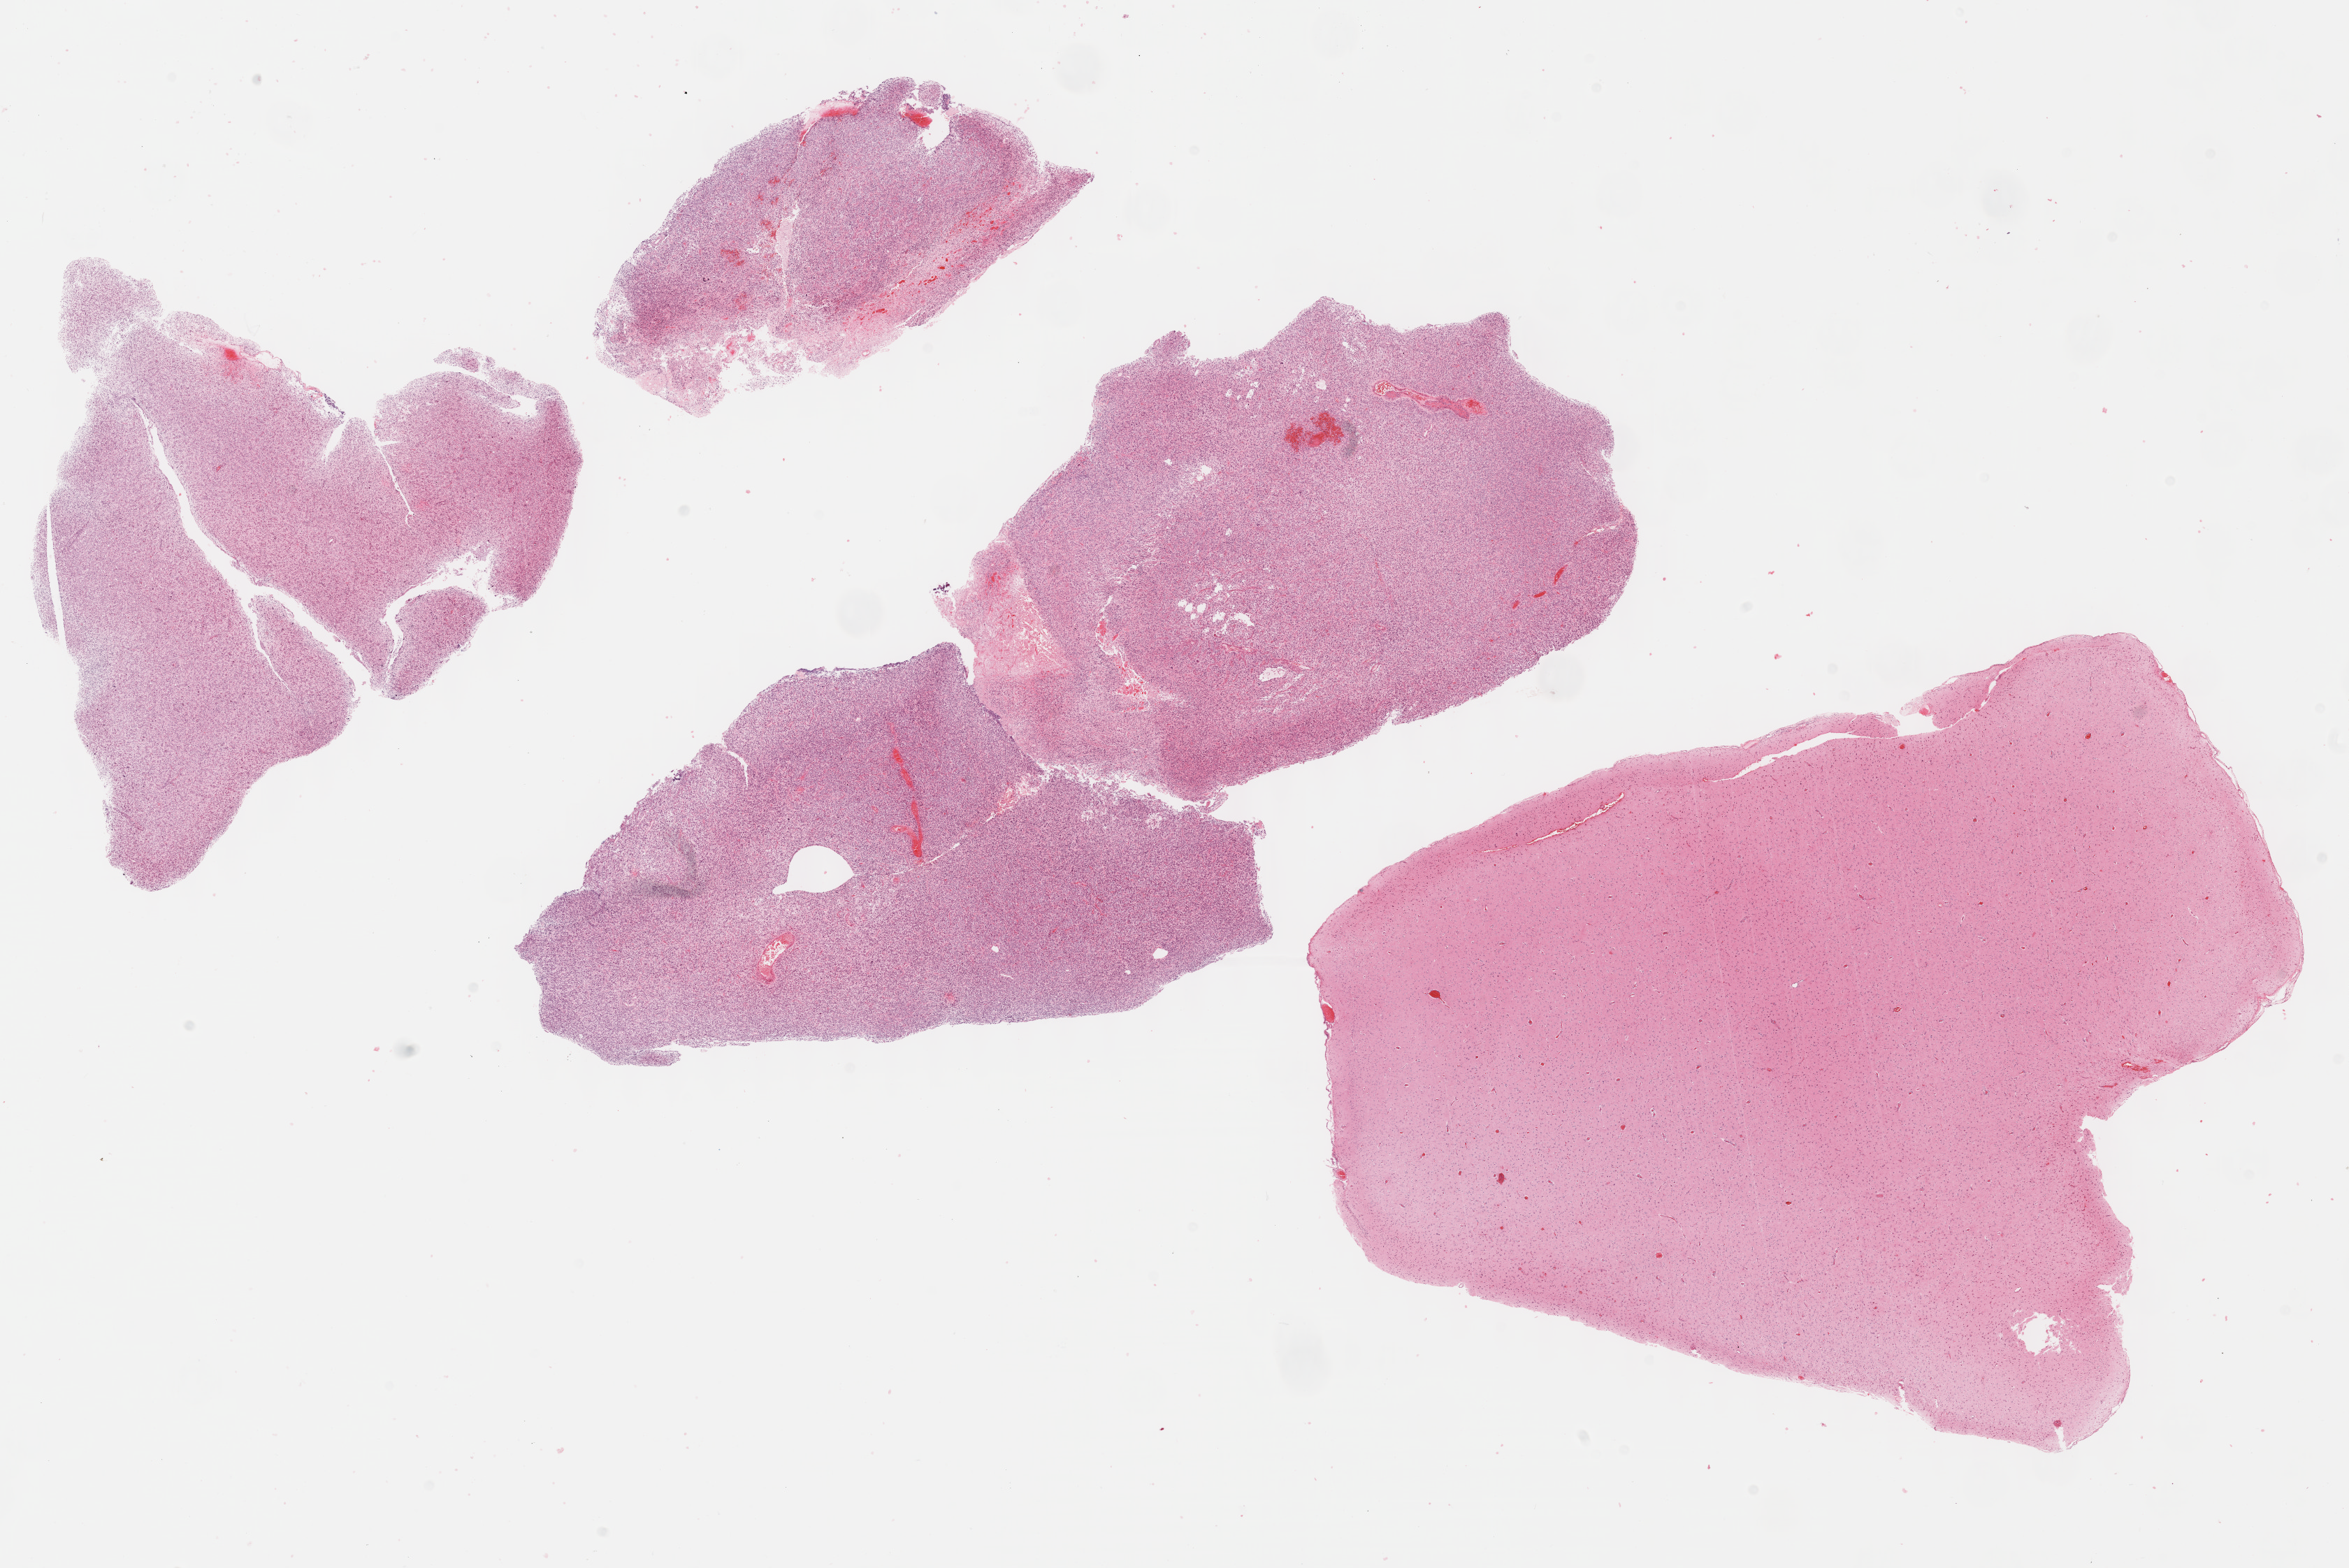
H&E whole-slide image — low-resolution overview of the scanned area, about 27.2 x 18.1 mm; formalin-fixed paraffin-embedded (FFPE) diagnostic section; brain, primary tumour sample. Patient: male, age at initial diagnosis 59 years.
- diagnosis: Glioblastoma